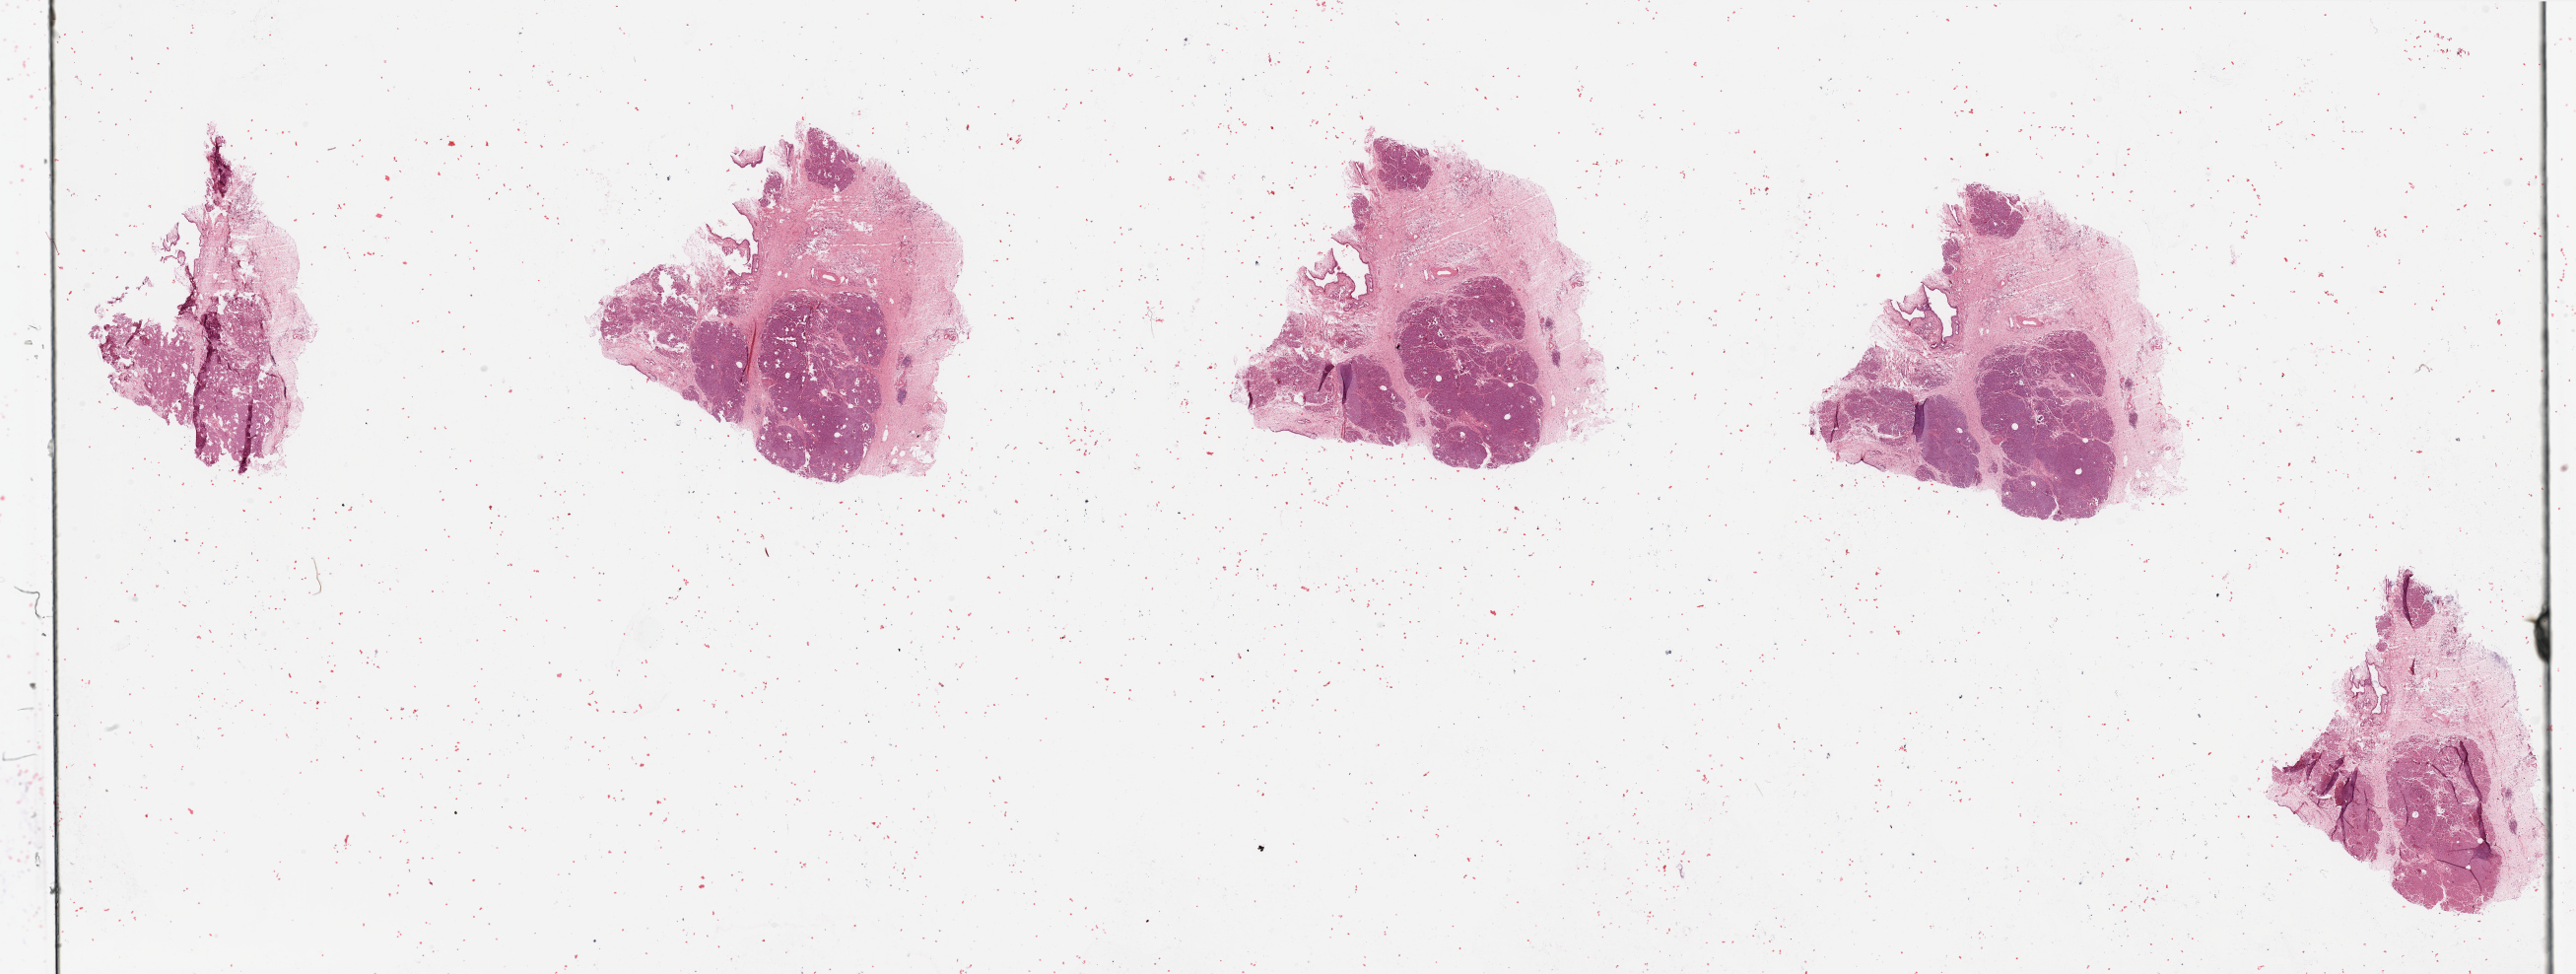
Digitized H&E-stained tissue section (whole slide), shown as a low-resolution overview of the whole scanned area (about 41.3 x 15.6 mm, slide scanned at 20x). Pancreas, normal (non-tumour) tissue. Male, 61 y/o.
This section: normal (non-tumour) tissue from the same patient. Patient diagnosis: Infiltrating duct carcinoma, NOS.